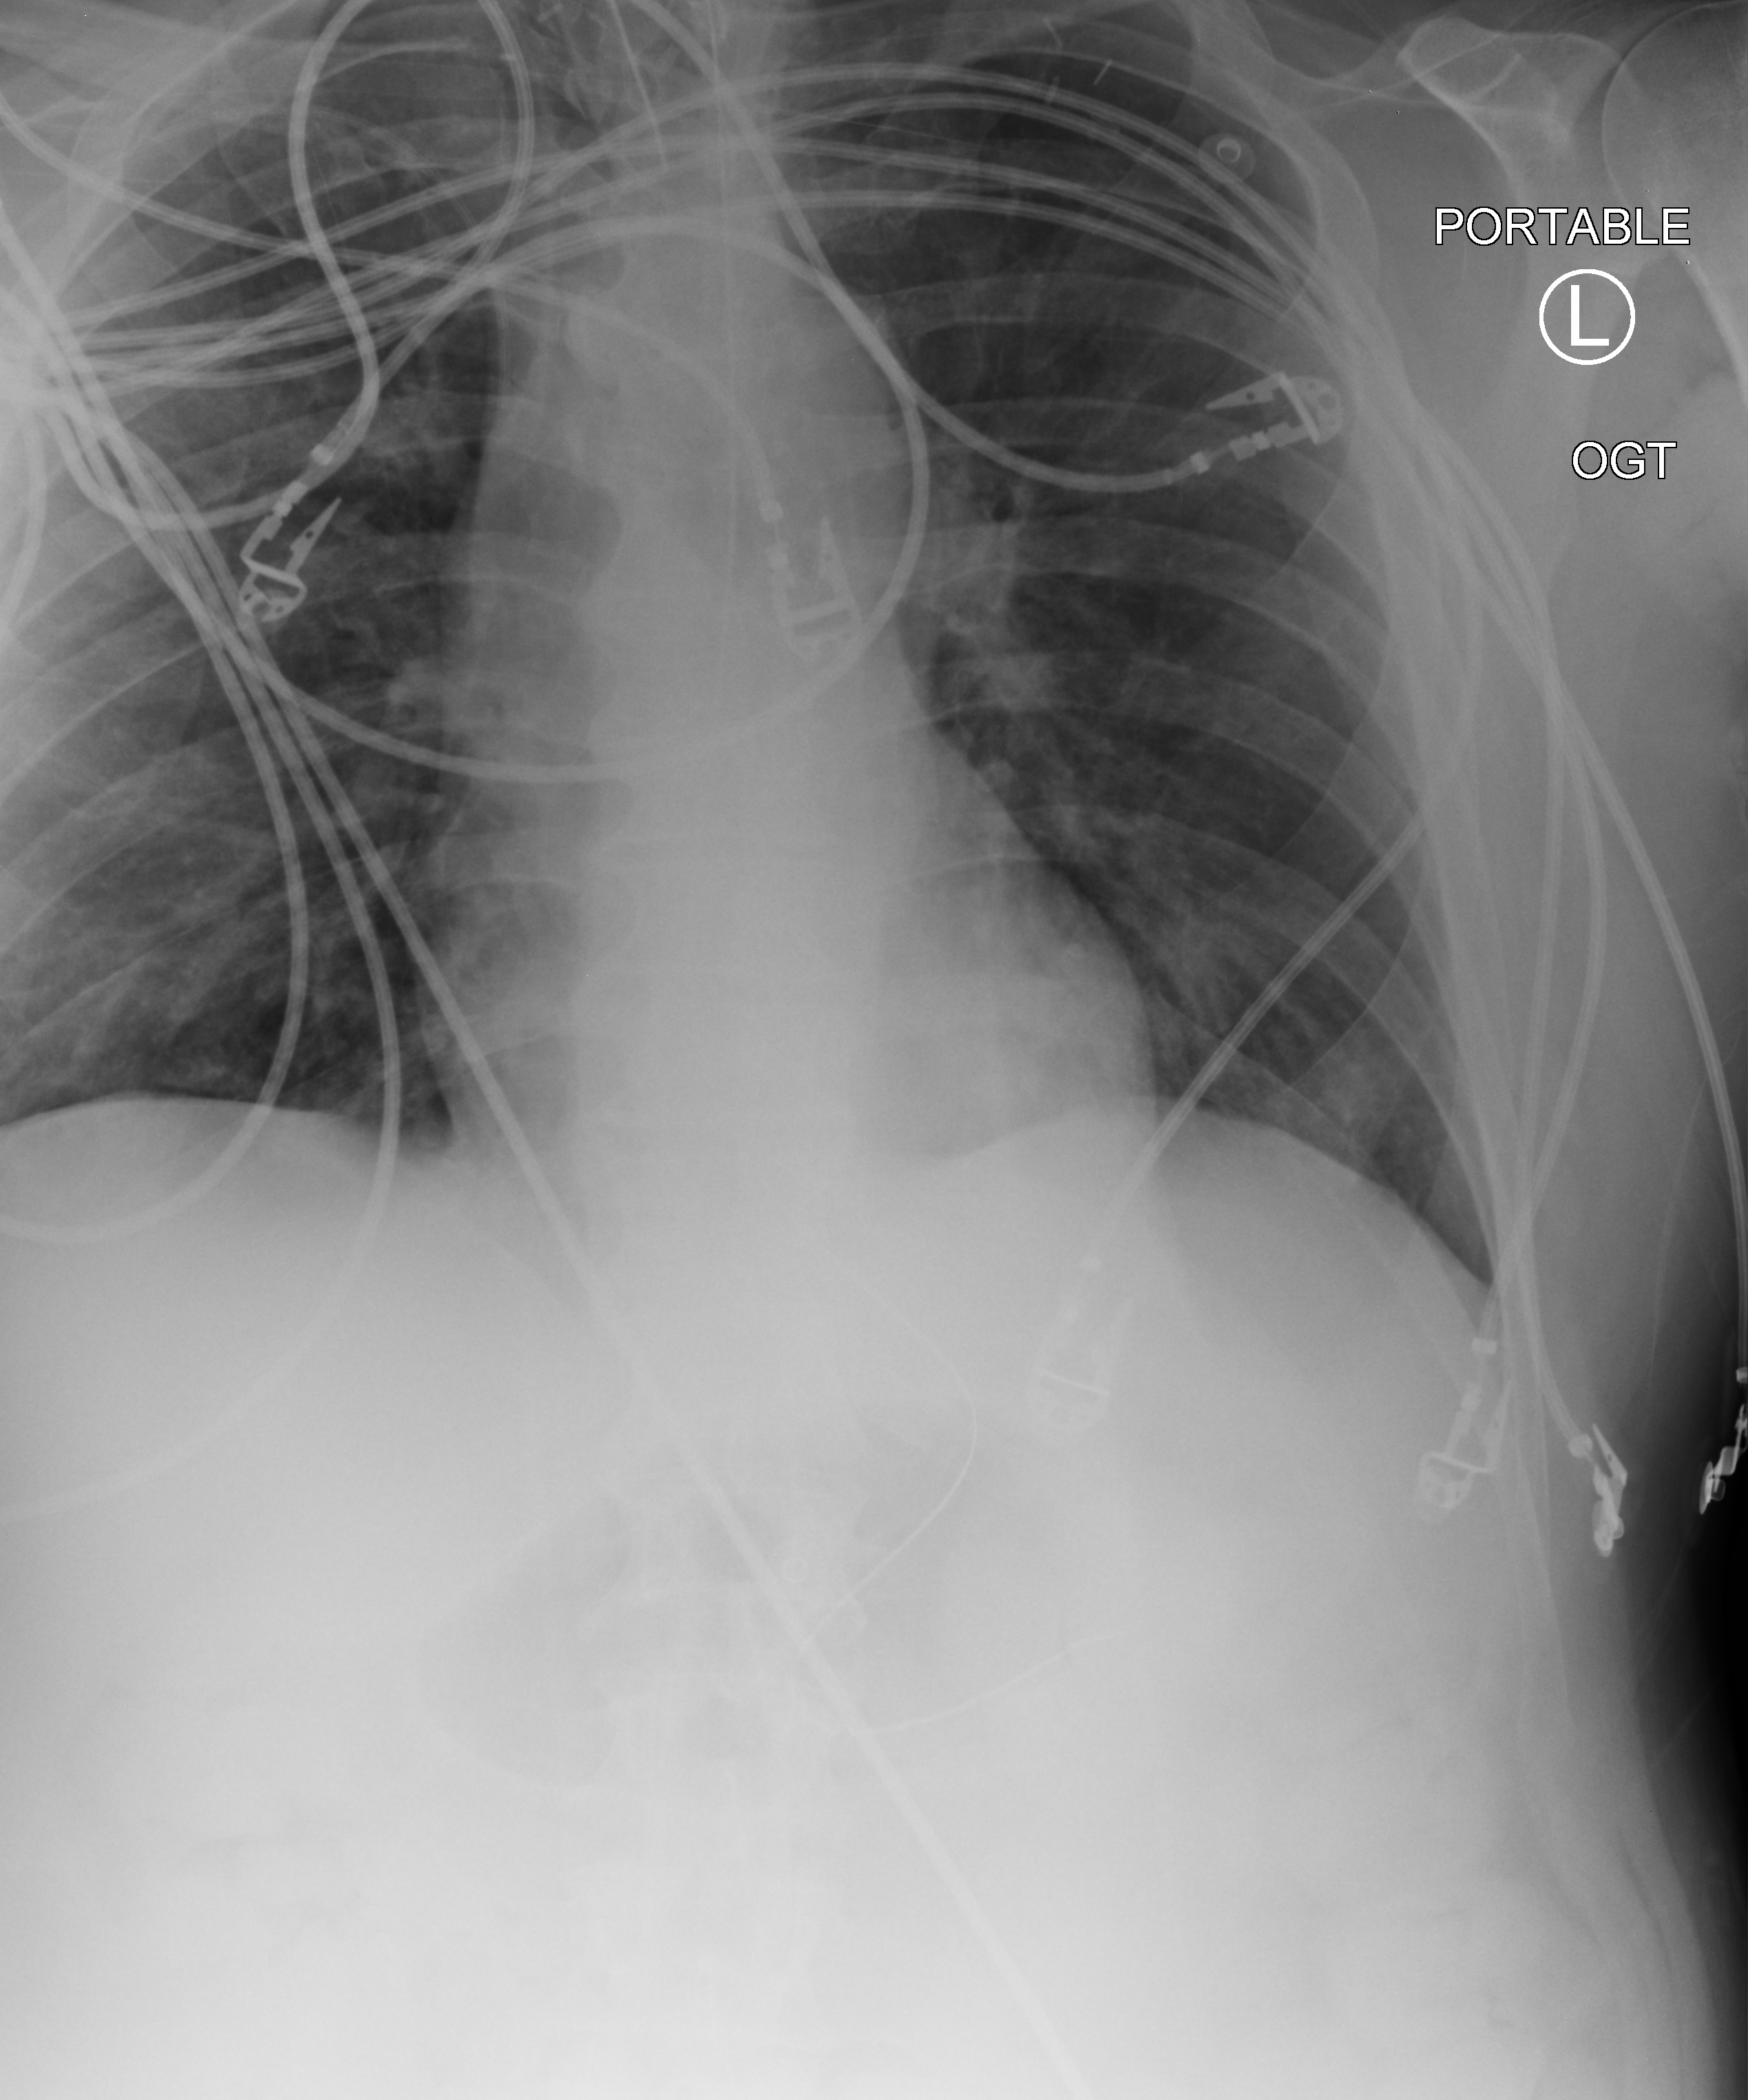
Bedside chest radiograph (computed radiography); anteroposterior (AP) projection. Patient hospitalised with COVID-19, aged 18–59 years.
From the hospital-stay record, not from the radiograph (when in the stay this image was taken is not recorded): admitted to intensive care during this hospital stay: yes; mechanically ventilated during this hospital stay: yes.